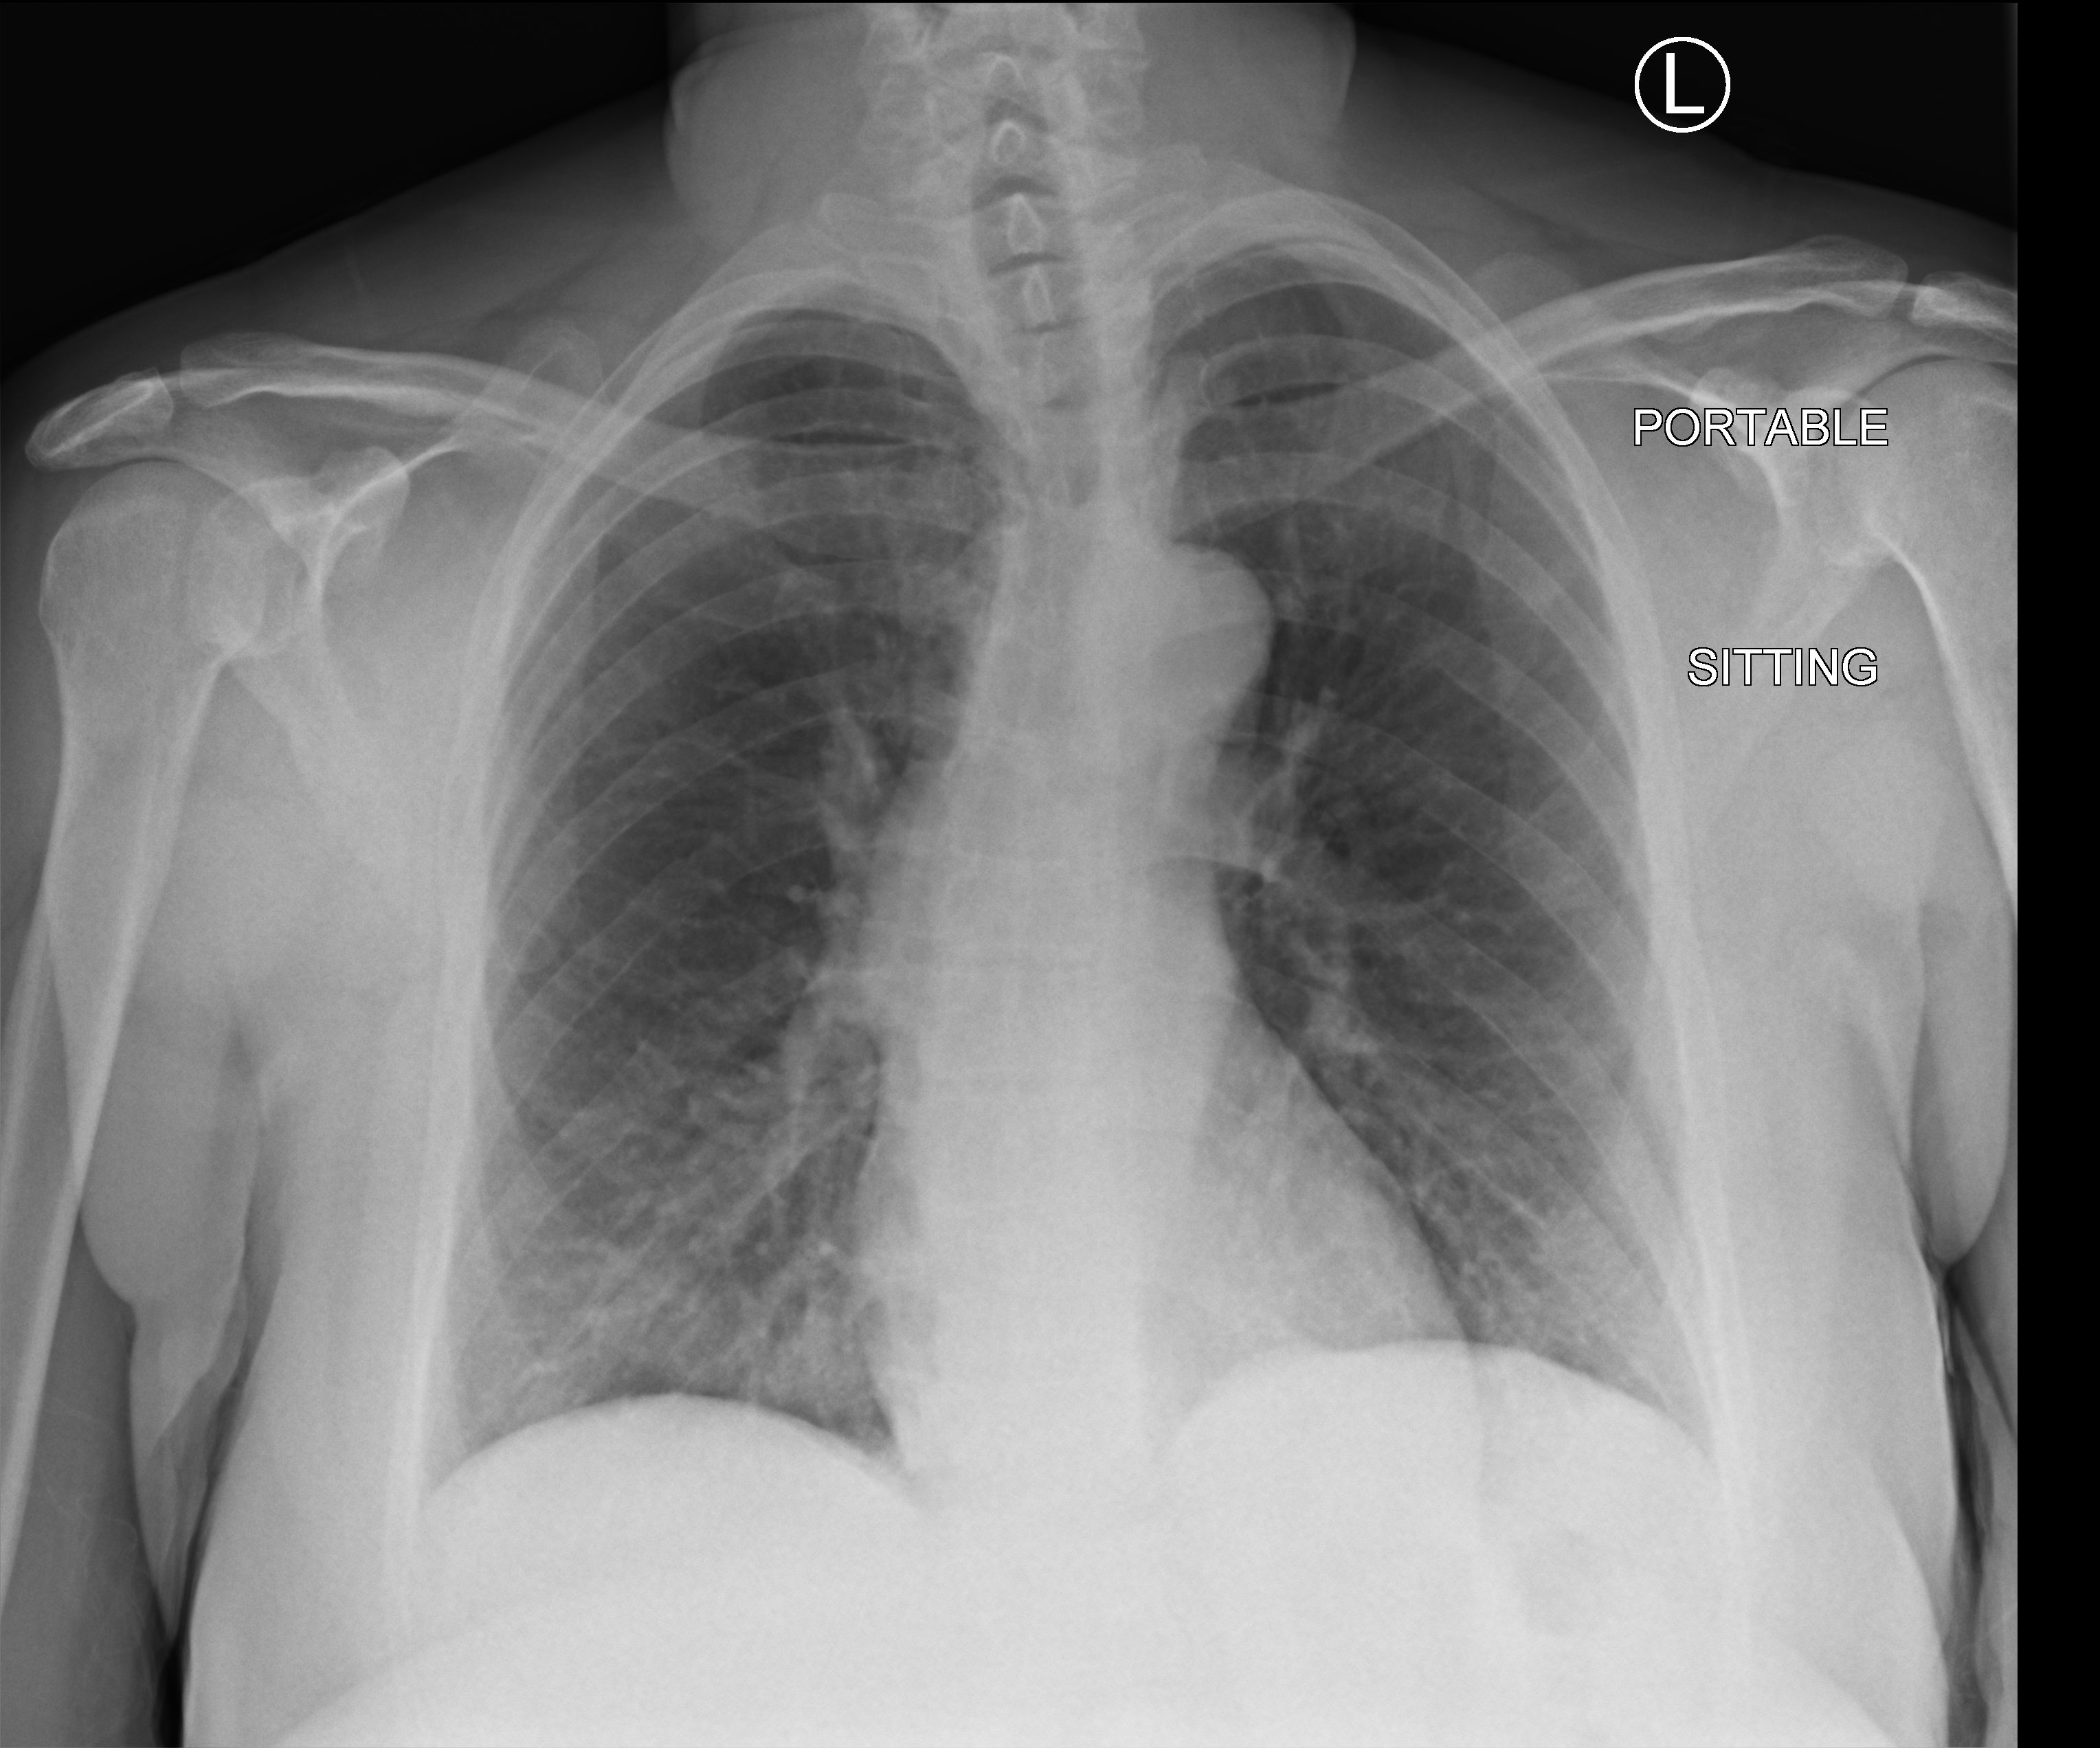
Bedside chest radiograph (computed radiography); anteroposterior (AP) projection. Patient hospitalised with COVID-19; female, aged 18–59 years.
Hospital-stay facts (about this admission, not read from this image; timing relative to this image not recorded): mechanically ventilated during this hospital stay: no.